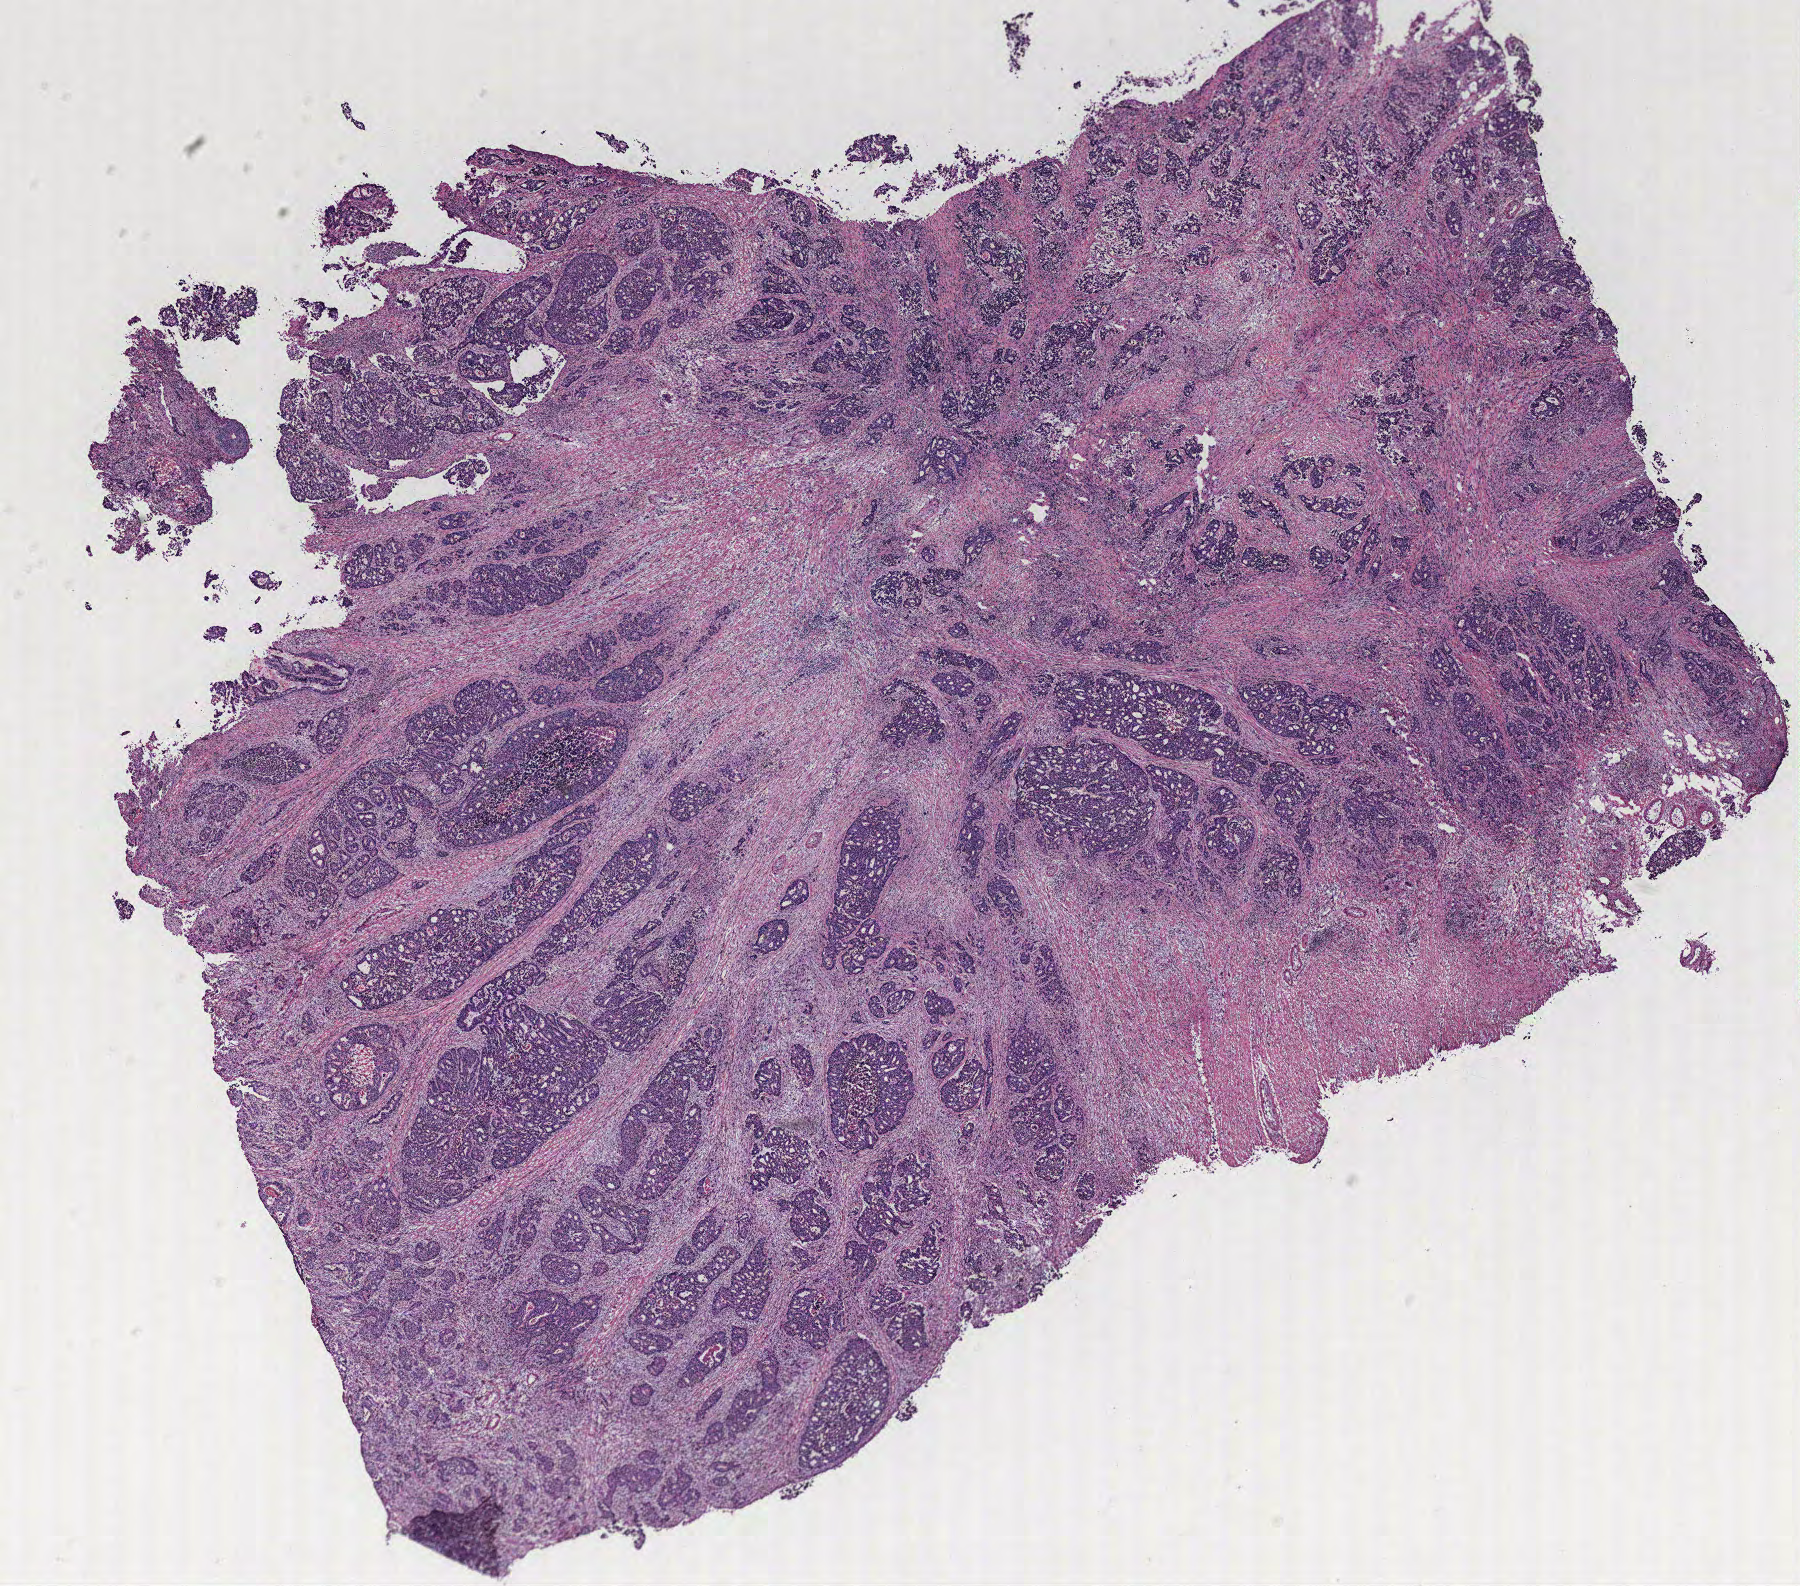
Whole-slide histology image, H&E-stained — shown as a low-resolution overview of the whole scanned area (about 14.4 x 12.7 mm, acquisition: 40x scan). Tumour tissue sample, colon. Male, 64 y/o.
Primary tumour site (as recorded): colon. AJCC pathologic stage: IVA. Diagnosis: Adenocarcinoma, NOS.